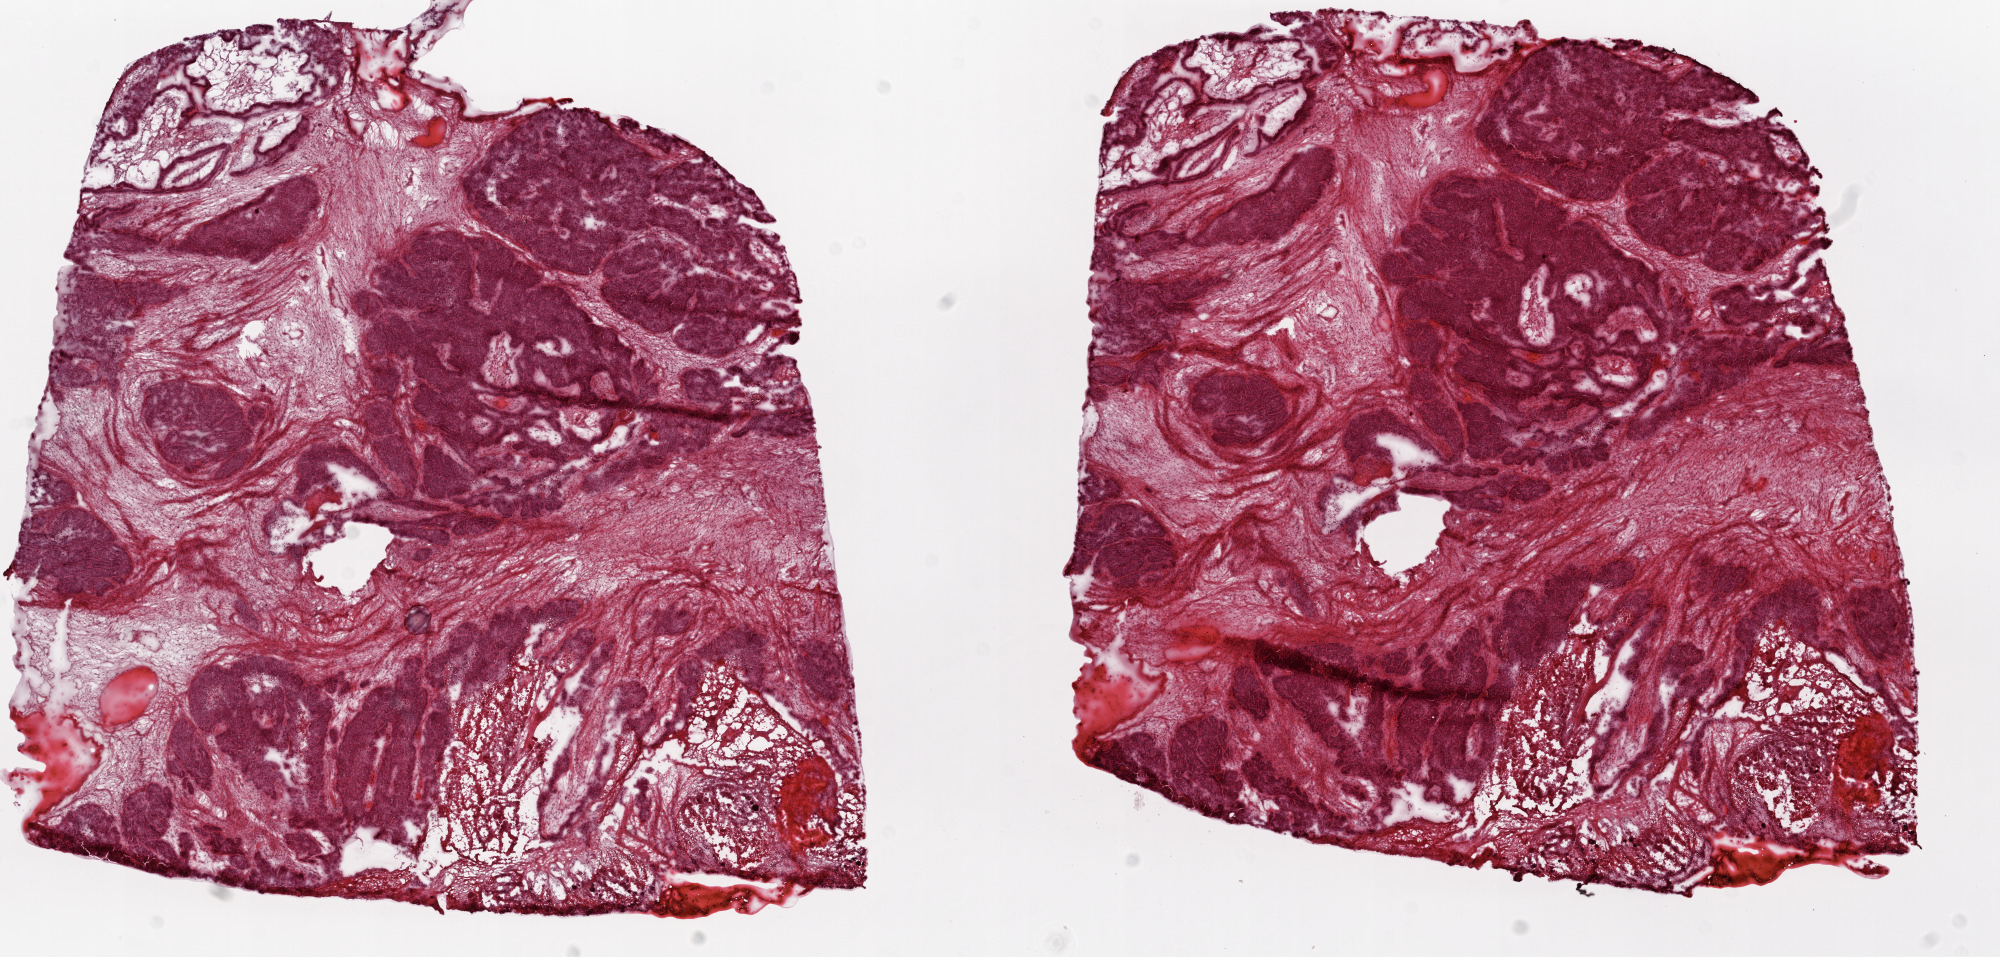
Hematoxylin and eosin (H&E) stained whole-slide image — shown as a low-resolution overview of the whole scanned area (about 16.0 x 7.7 mm), frozen section from the top of the tissue portion, ovary, primary tumour sample. Female patient; age at initial diagnosis 56 years. Histologic grade: G3 (poorly differentiated). Slide review estimates, as recorded: tumour cells 60%, tumour nuclei 70%, normal cells 0%, stromal cells 35%, necrosis 5%.
- FIGO stage: IIIC
- pathologic diagnosis: Serous cystadenocarcinoma, NOS